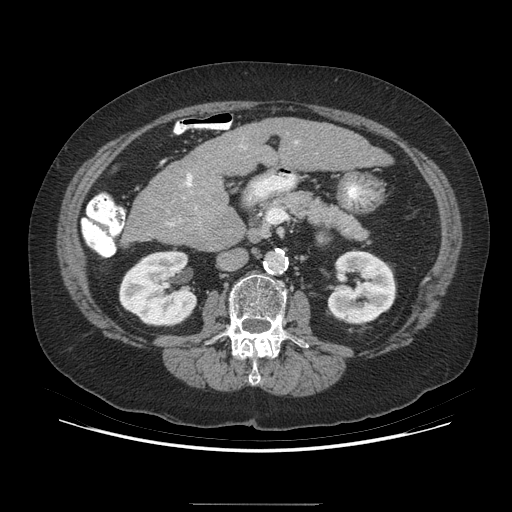
Contrast-enhanced abdominal CT (liver protocol), one axial slice. Position 138 of 192 along the scan axis. 140 kVp. Soft-tissue window (W 400 / L 40 HU). 512 × 512 image matrix, field of view 400 × 400 mm. Case-level facts recorded for this patient, not image findings: diagnosis: hepatocellular carcinoma (patient treated with transarterial chemoembolisation; whether this scan precedes or follows treatment is not stated here); TNM stage (as recorded): Stage-I; Child-Pugh class: A; tumour nodularity: uninodular; tumour size: 3.2 cm.
Structures marked on this image (semi-automatically segmented with operator editing):
- liver parenchyma outside the tumour (the mass and vessels are separate outlines, so this box may not span the whole liver): bounding box <126,118,391,249> (left, top, right, bottom; pixels)
- liver vessels: <167,141,298,226>